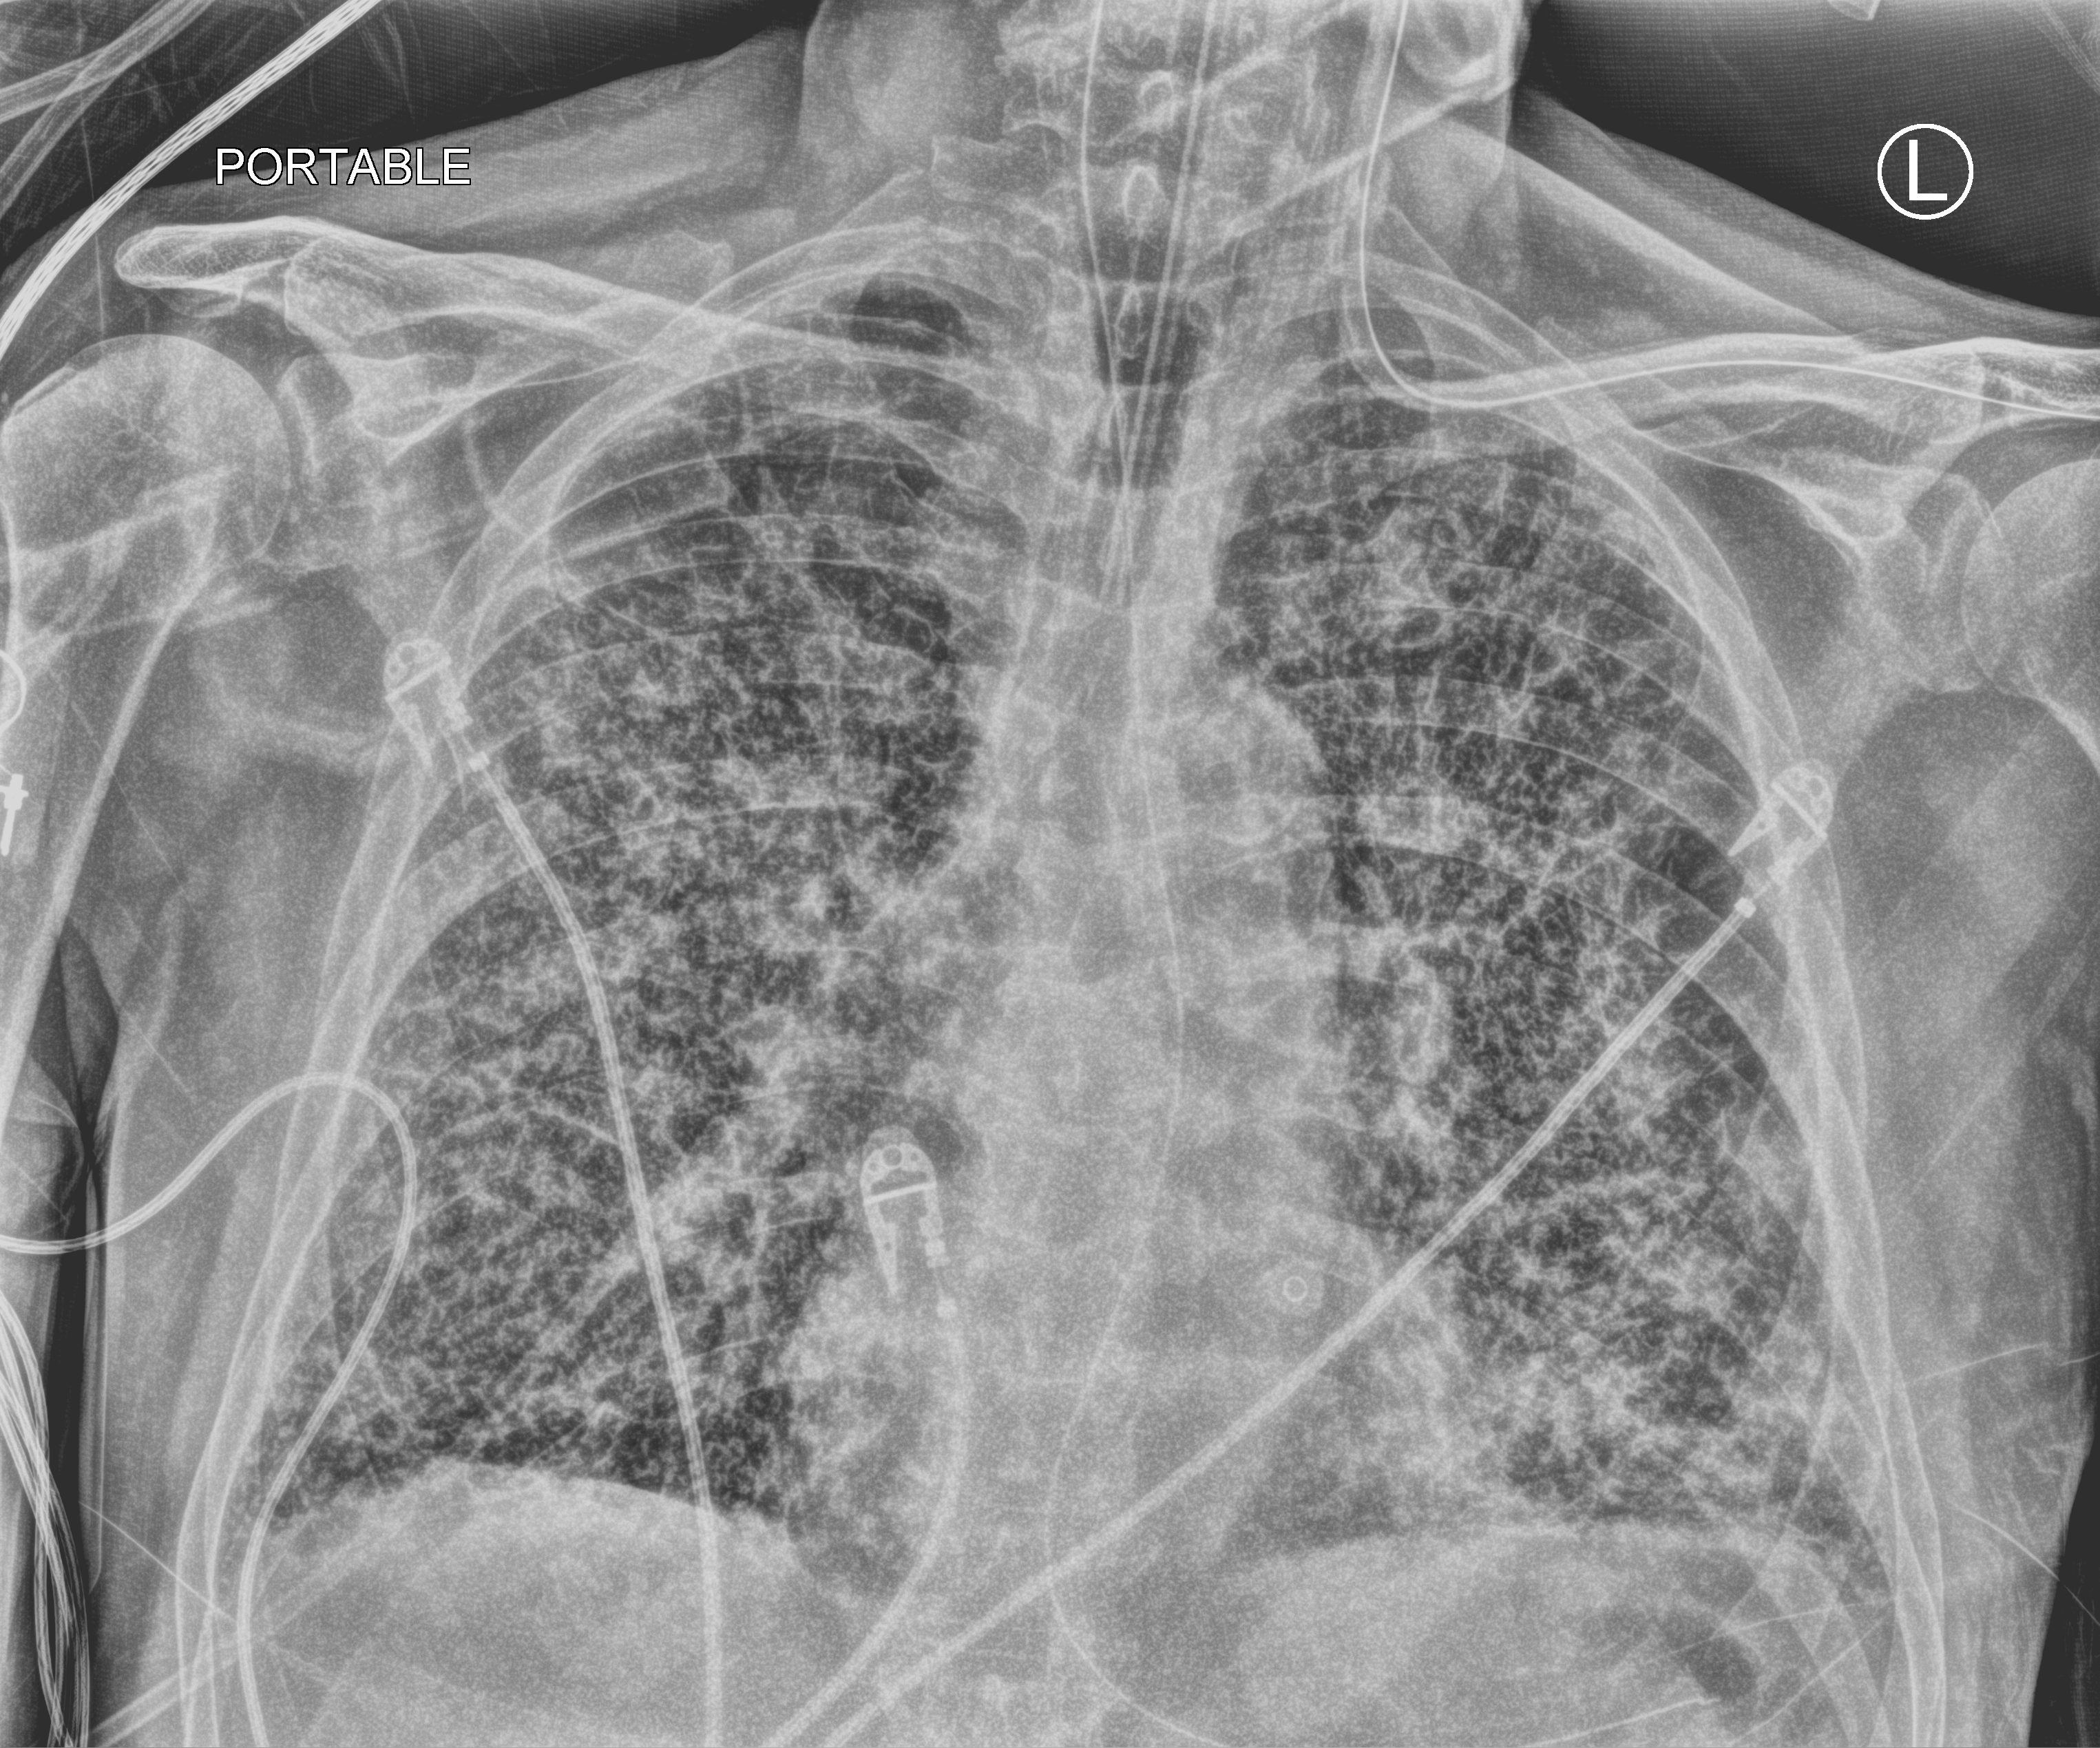
Portable chest radiograph; anteroposterior (AP) projection. Male patient hospitalised with COVID-19, age 75–90 years.
Admission-level facts for this patient (not findings on this image; timing relative to this image not recorded):
- admitted to intensive care during this hospital stay: yes
- mechanically ventilated during this hospital stay: yes